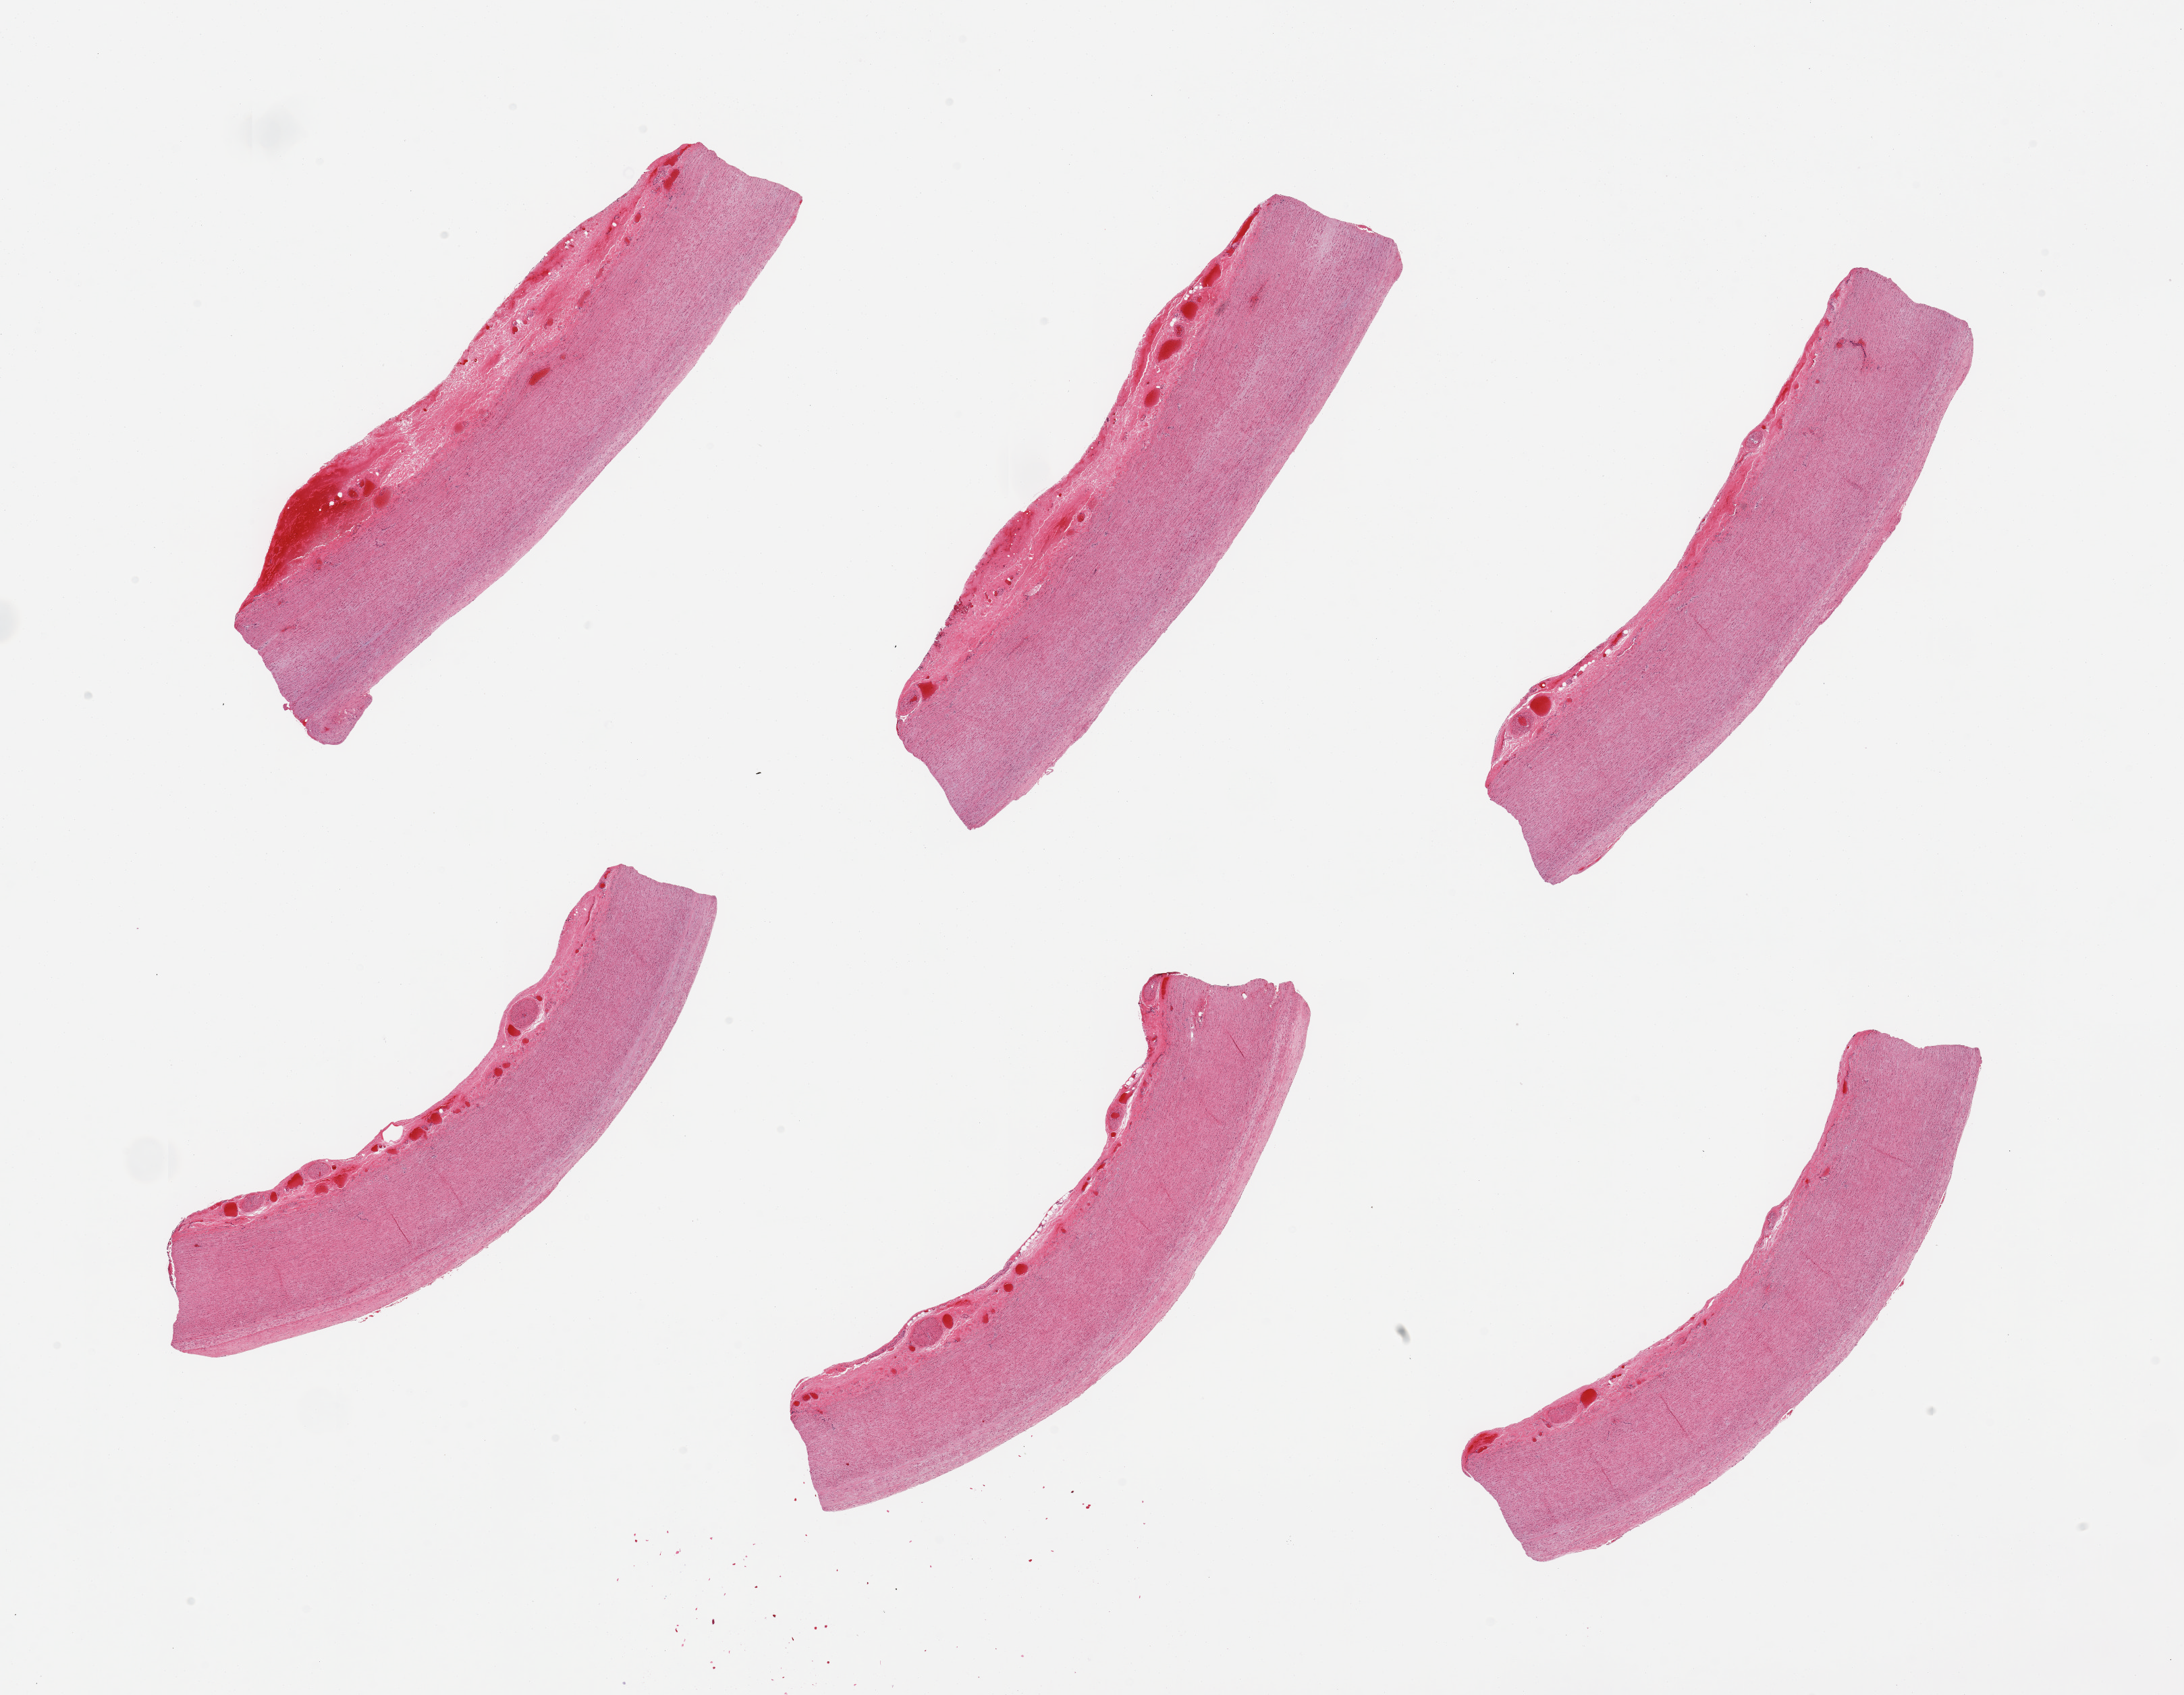
Hematoxylin and eosin (H&E) whole-slide image, a low-resolution overview of the entire scanned area, about 25.6 x 19.9 mm; PAXgene-fixed paraffin-embedded (PFPE) section; sampled site (target tissue): aorta; donor tissue sample.
Review note (as recorded): 6 pieces; mild to moderate atherosclerosis; congested adventitia measures up to 0.8mm.